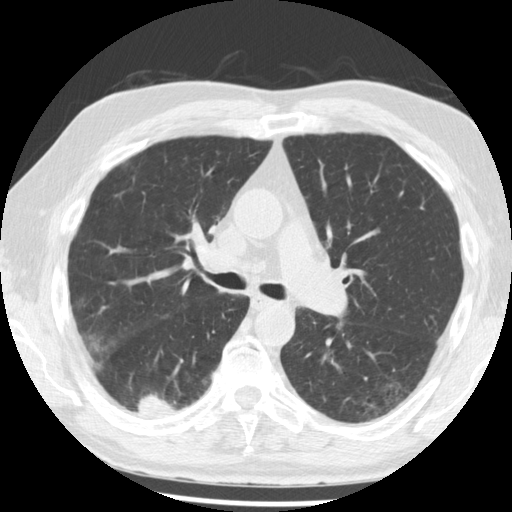
Low-dose screening chest CT, one axial slice; slice 128 of 221 in the series (ordered by position); reconstruction kernel STANDARD; 120 kVp; lung window (W 1500 / L -600 HU); 2.5 mm slice thickness; 512 × 512 image matrix, field of view 350 × 350 mm.
Annotated regions visible in this slice (outlined manually by an expert reader):
- lesion 1 (tumor, lower lobe of right lung): box from (x=138, y=394) to (x=182, y=415) px